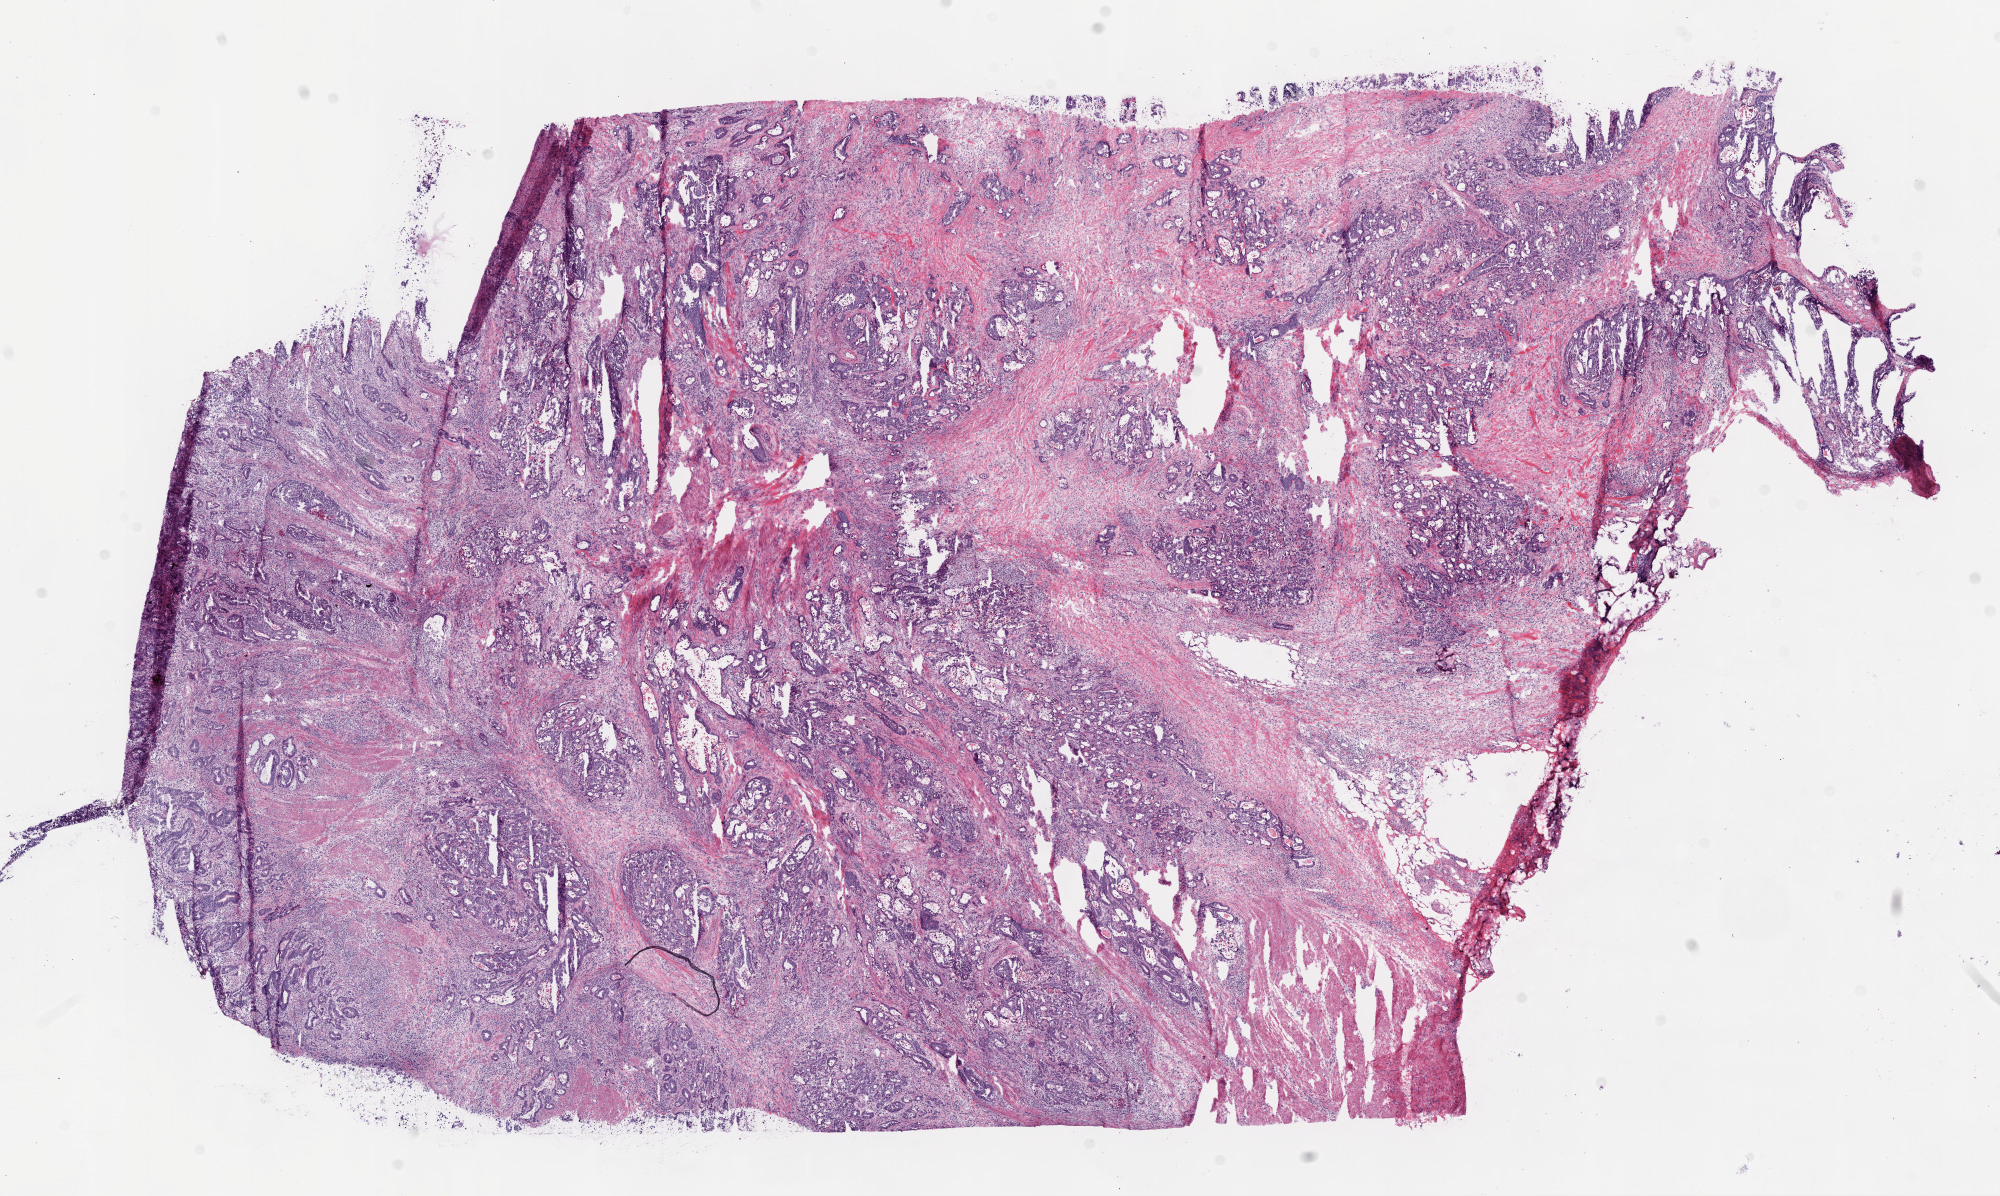
Whole-slide histology image, H&E, low-resolution overview of the scanned area, about 16.0 x 9.6 mm (acquisition: 20x scan), frozen section from the bottom of the tissue portion, rectum, primary tumour sample. Female, age 76 years at initial diagnosis. Pathologist review of this section (percent, as recorded): tumour cells 70%, tumour nuclei 70%, normal cells 15%, stromal cells 15%, necrosis 0%.
- lymph nodes positive (case pathology): 3 of 24 examined
- AJCC pathologic stage: IIIC (6th edition)
- diagnosis: Adenocarcinoma, NOS